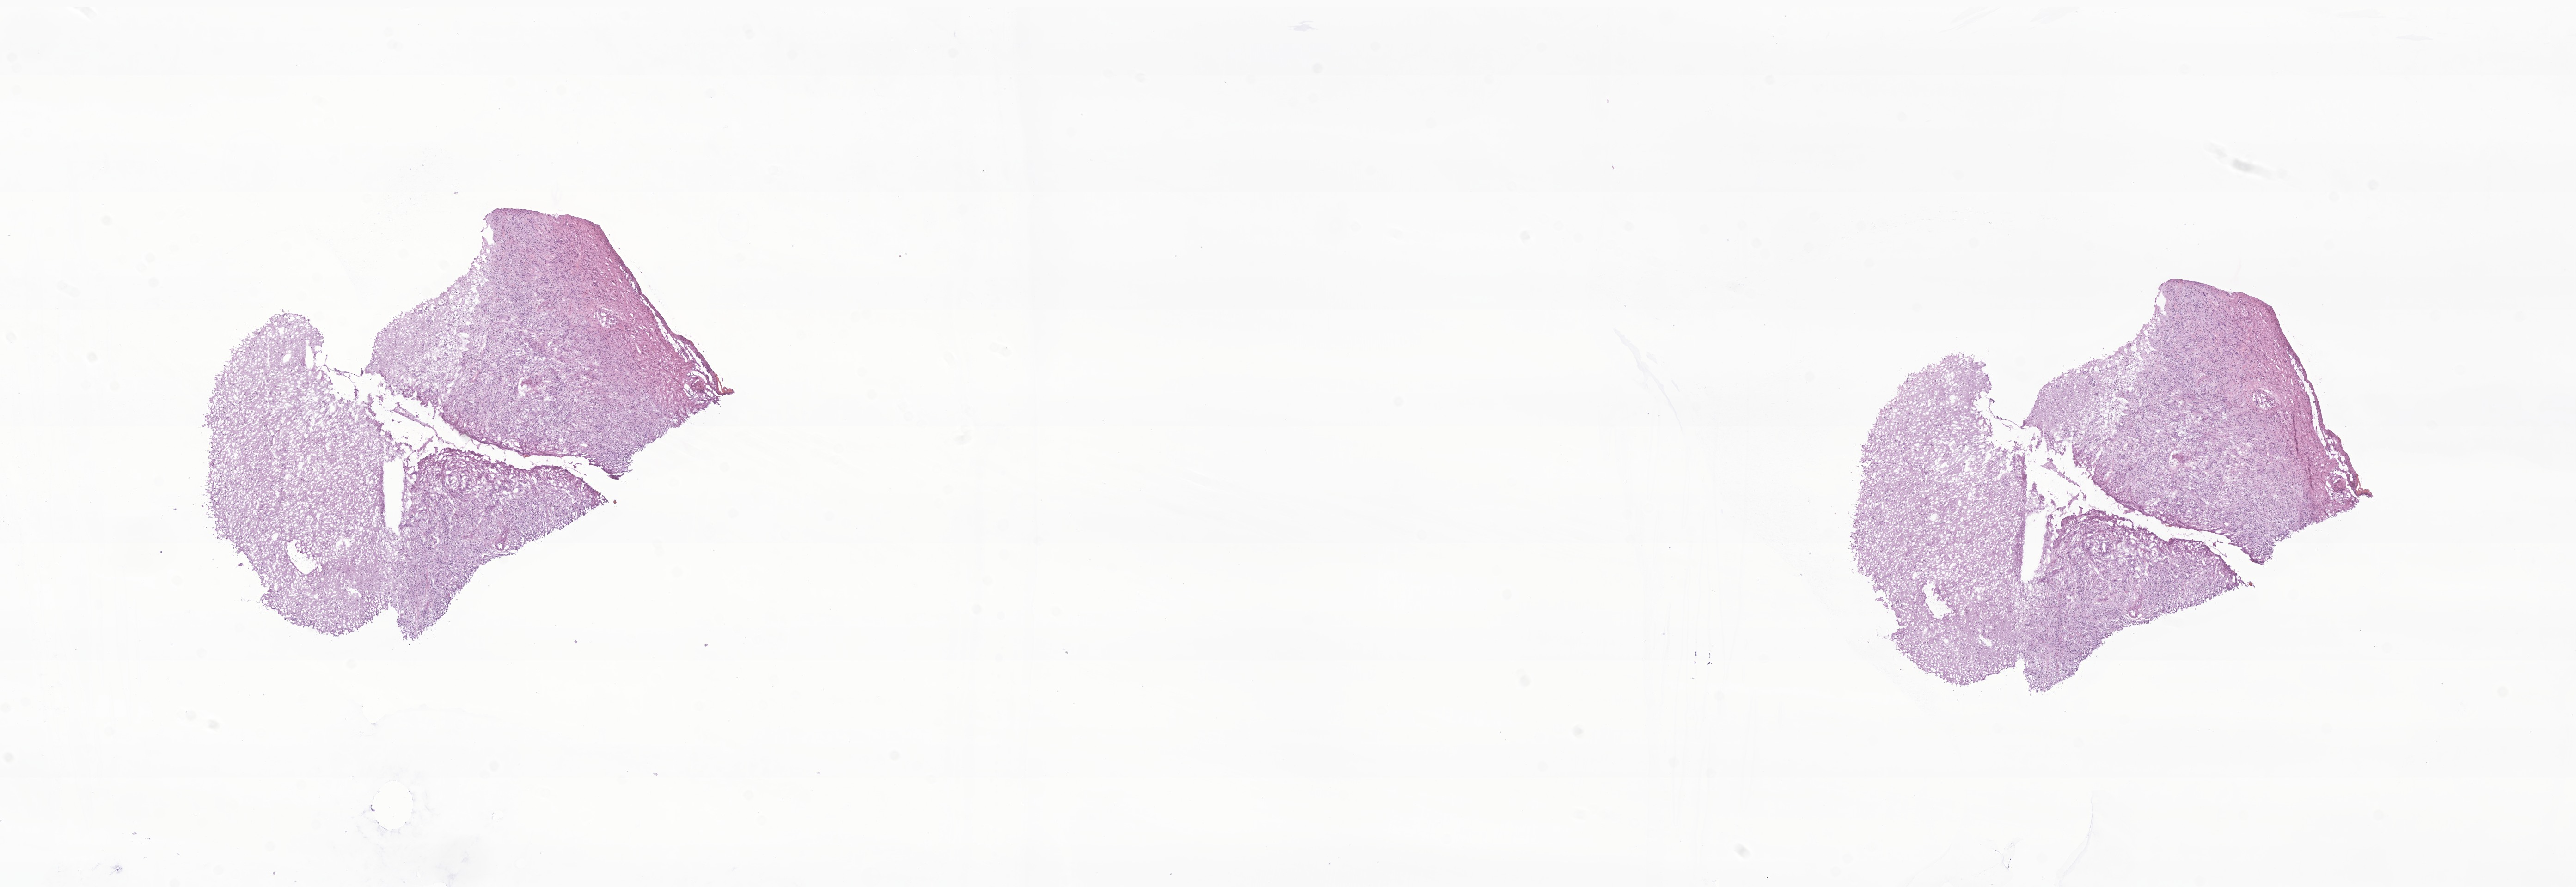
Whole-slide image, hematoxylin and eosin (H&E) stain of tumor tissue from the temporal lobe, whole scanned area (about 23.5 x 8.1 mm) shown as a low-resolution overview, cryosection (OCT / tissue freezing medium). Patient male; age 183 months (15 years 3 months).
Diagnosis: Ganglioglioma, NOS.